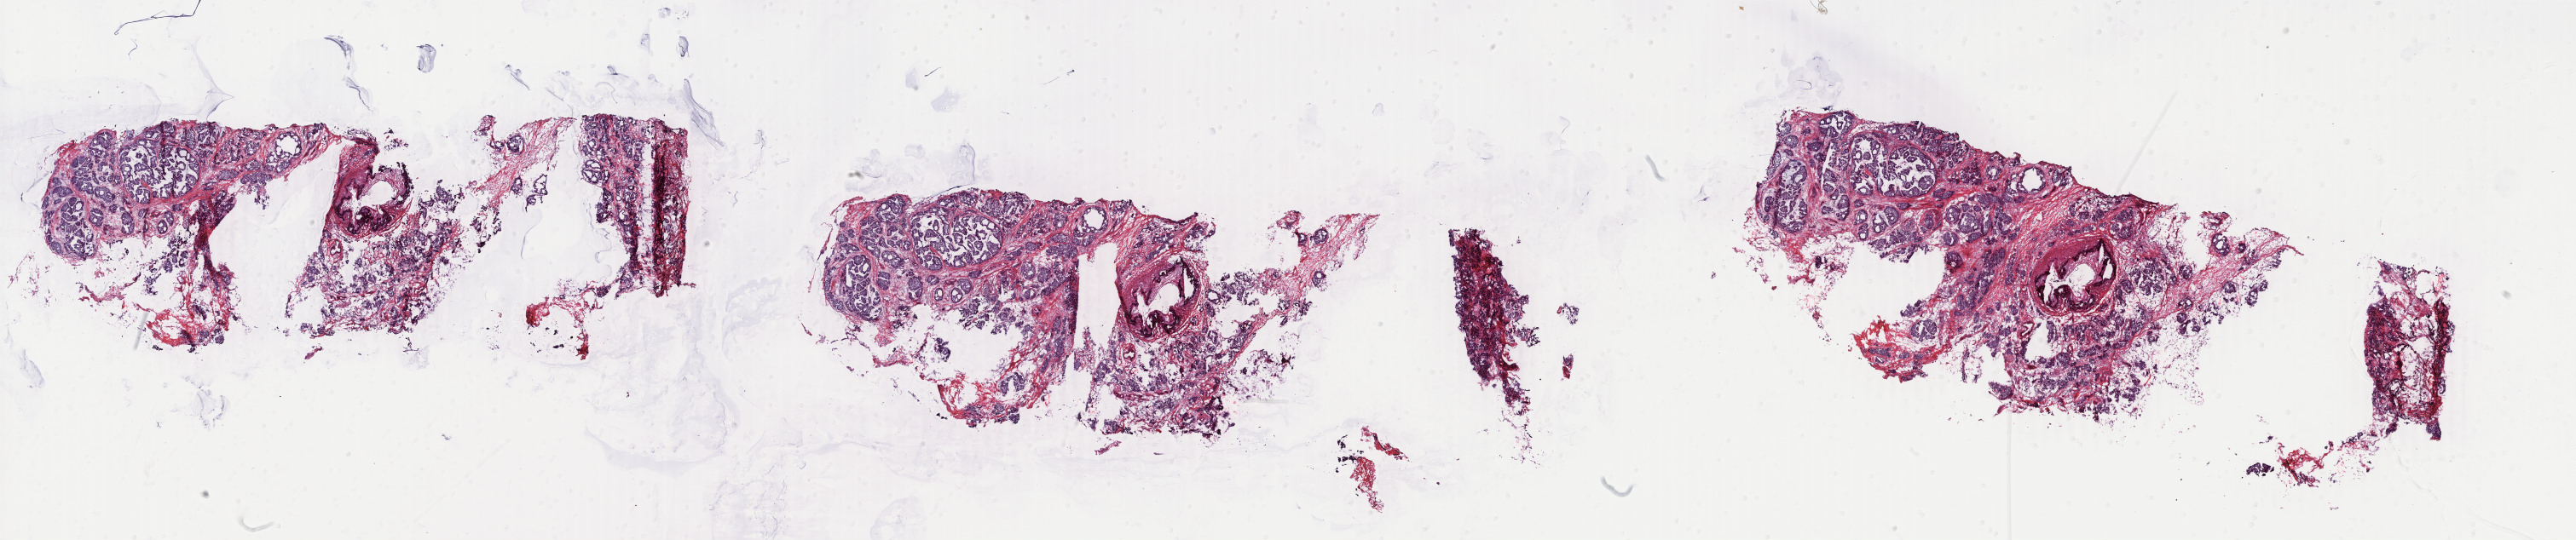
Digitized H&E-stained tissue section (whole slide) — low-resolution overview of the scanned area, about 48.1 x 10.1 mm (acquisition: 40x scan), frozen section, primary tumour sample from the breast. Patient: female, age at initial diagnosis 73 years. Slide review estimates, as recorded: tumour cells 80%, tumour nuclei 85%, normal cells 5%, stromal cells 15%, necrosis 0%. Inflammatory infiltration, as recorded: lymphocyte infiltration 0%, monocyte infiltration 0%, neutrophil infiltration 0%.
• laterality: right
• AJCC pathologic stage: IIA (6th edition)
• lymph nodes positive (case pathology): 0 of 1 examined
• pathologic diagnosis: Infiltrating duct carcinoma, NOS